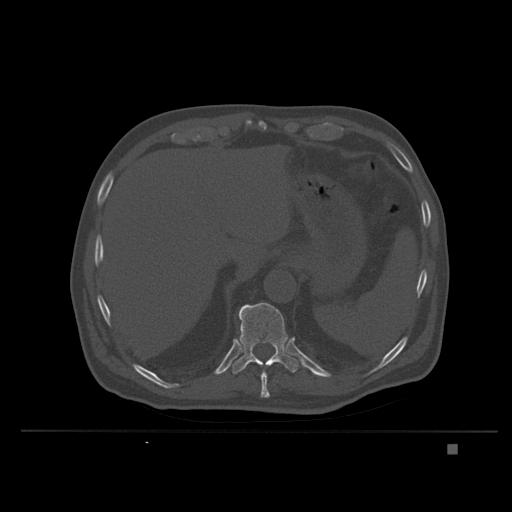
CT including the spine, one axial slice; slice 182 of 435 in the series (ordered by position); bone window (W 1800 / L 400 HU); 512 × 512 image matrix, field of view 434 × 434 mm. Male patient, age 73 years. Case-level facts recorded for this patient, not image findings: primary cancer: skin.
Outlined on this slice (semi-automatic segmentation, software-assisted and operator-edited):
- T10 vertebra: bounding box <261,365,270,397> (left, top, right, bottom; pixels)
- T11 vertebra: <232,303,299,374>
- T9 vertebra: <262,395,270,398>